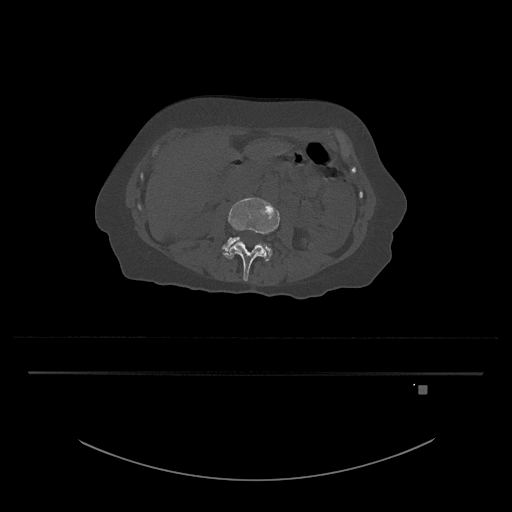
CT including the spine, one axial slice. Position 410 of 797 along the scan axis. Reconstruction kernel Br40s/3. 120 kVp. Bone window (W 1800 / L 400 HU). 512 × 512 image matrix, field of view 500 × 500 mm. Female patient, age 57 years. Case-level facts recorded for this patient, not image findings: primary cancer: cervical.
Outlined on this slice (semi-automatically segmented with operator editing):
- L3 vertebra: bounding box (x1, y1, x2, y2) in pixels: (223, 197, 280, 281)
- L4 vertebra: (222, 237, 272, 261)